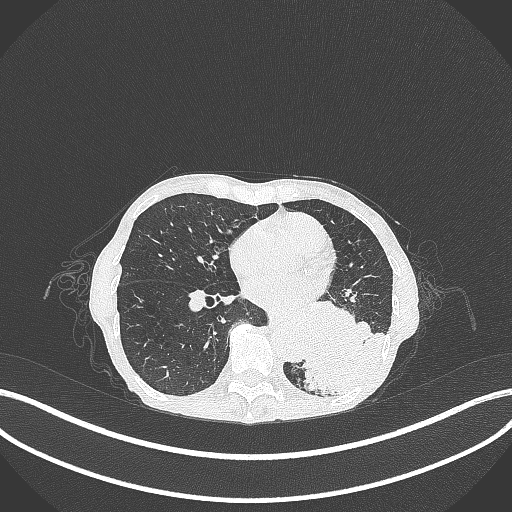
Chest CT, one axial slice. Slice 111 of 347 in the series (ordered by position). Reconstruction kernel B70f. 120 kVp. Lung window (W 1500 / L -600 HU). 512 × 512 image matrix, field of view 400 × 400 mm. Patient: female, 70 years. Case-level facts recorded for this patient, not image findings: clinical TNM (as recorded): T3 N0 M0; histopathological grade: G3.
Outlined on this slice (bounding box drawn by a radiologist):
- lung tumour (recorded histology: small cell carcinoma): bounding box [x1, y1, x2, y2] px = [291, 310, 386, 398]